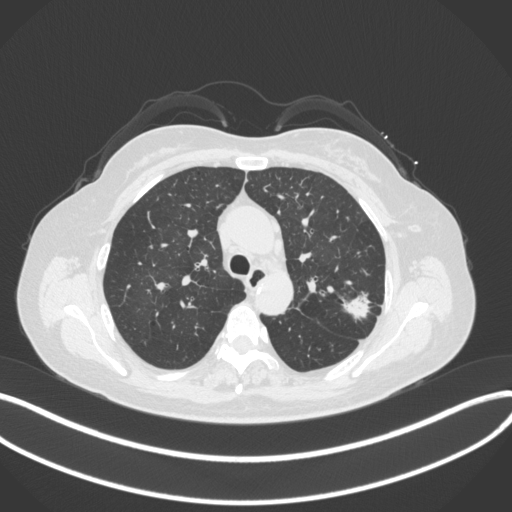
Chest CT, one axial slice; slice 240 of 330 in the series (ordered by position); reconstruction kernel B31f; 120 kVp; lung window (W 1500 / L -600 HU); 1 mm slice thickness; 512 × 512 image matrix, field of view 400 × 400 mm. Female patient, age 60 years. From the clinical record (not read from this slice): clinical TNM (as recorded): T1c N0 M0.
Outlined on this slice (bounding box drawn by a radiologist):
- lung tumour (recorded histology: adenocarcinoma): box from (x=342, y=286) to (x=375, y=324) px